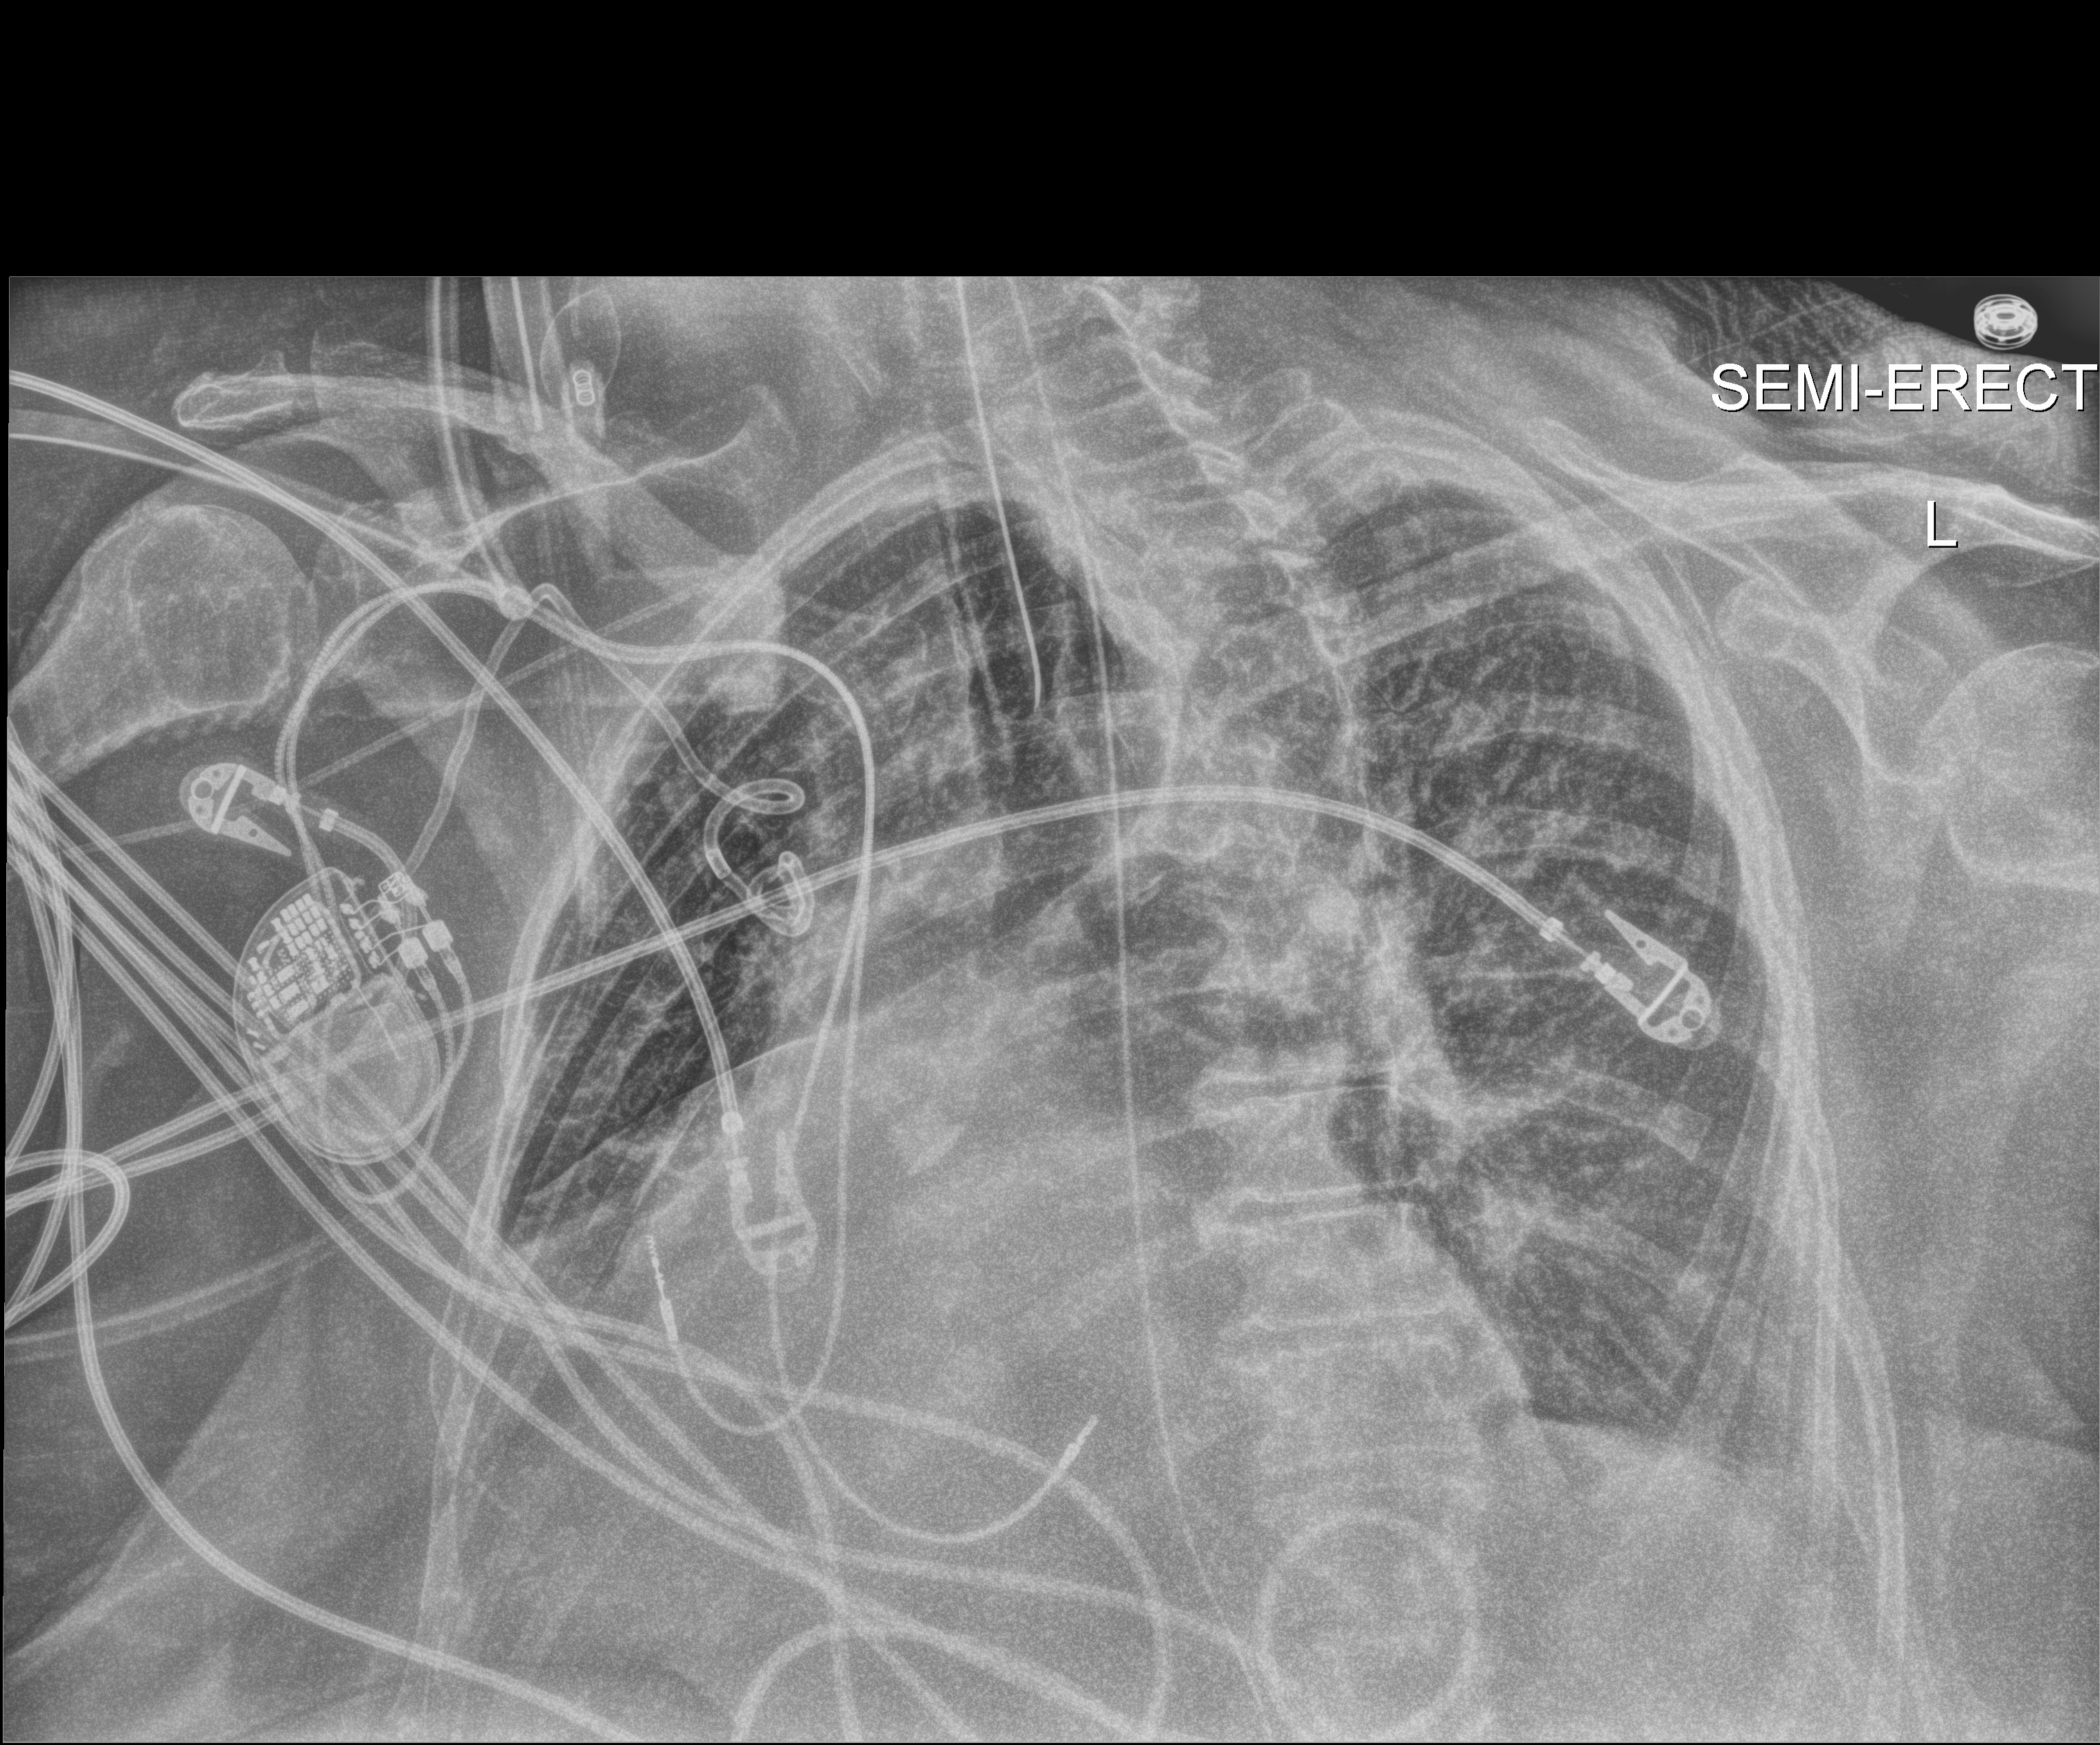
Portable chest radiograph; anteroposterior (AP) projection. Female patient hospitalised with COVID-19, age 75–90 years.
From the hospital-stay record, not from the radiograph (when in the stay this image was taken is not recorded): mechanically ventilated during this hospital stay: yes; smoking status (admission record): former.